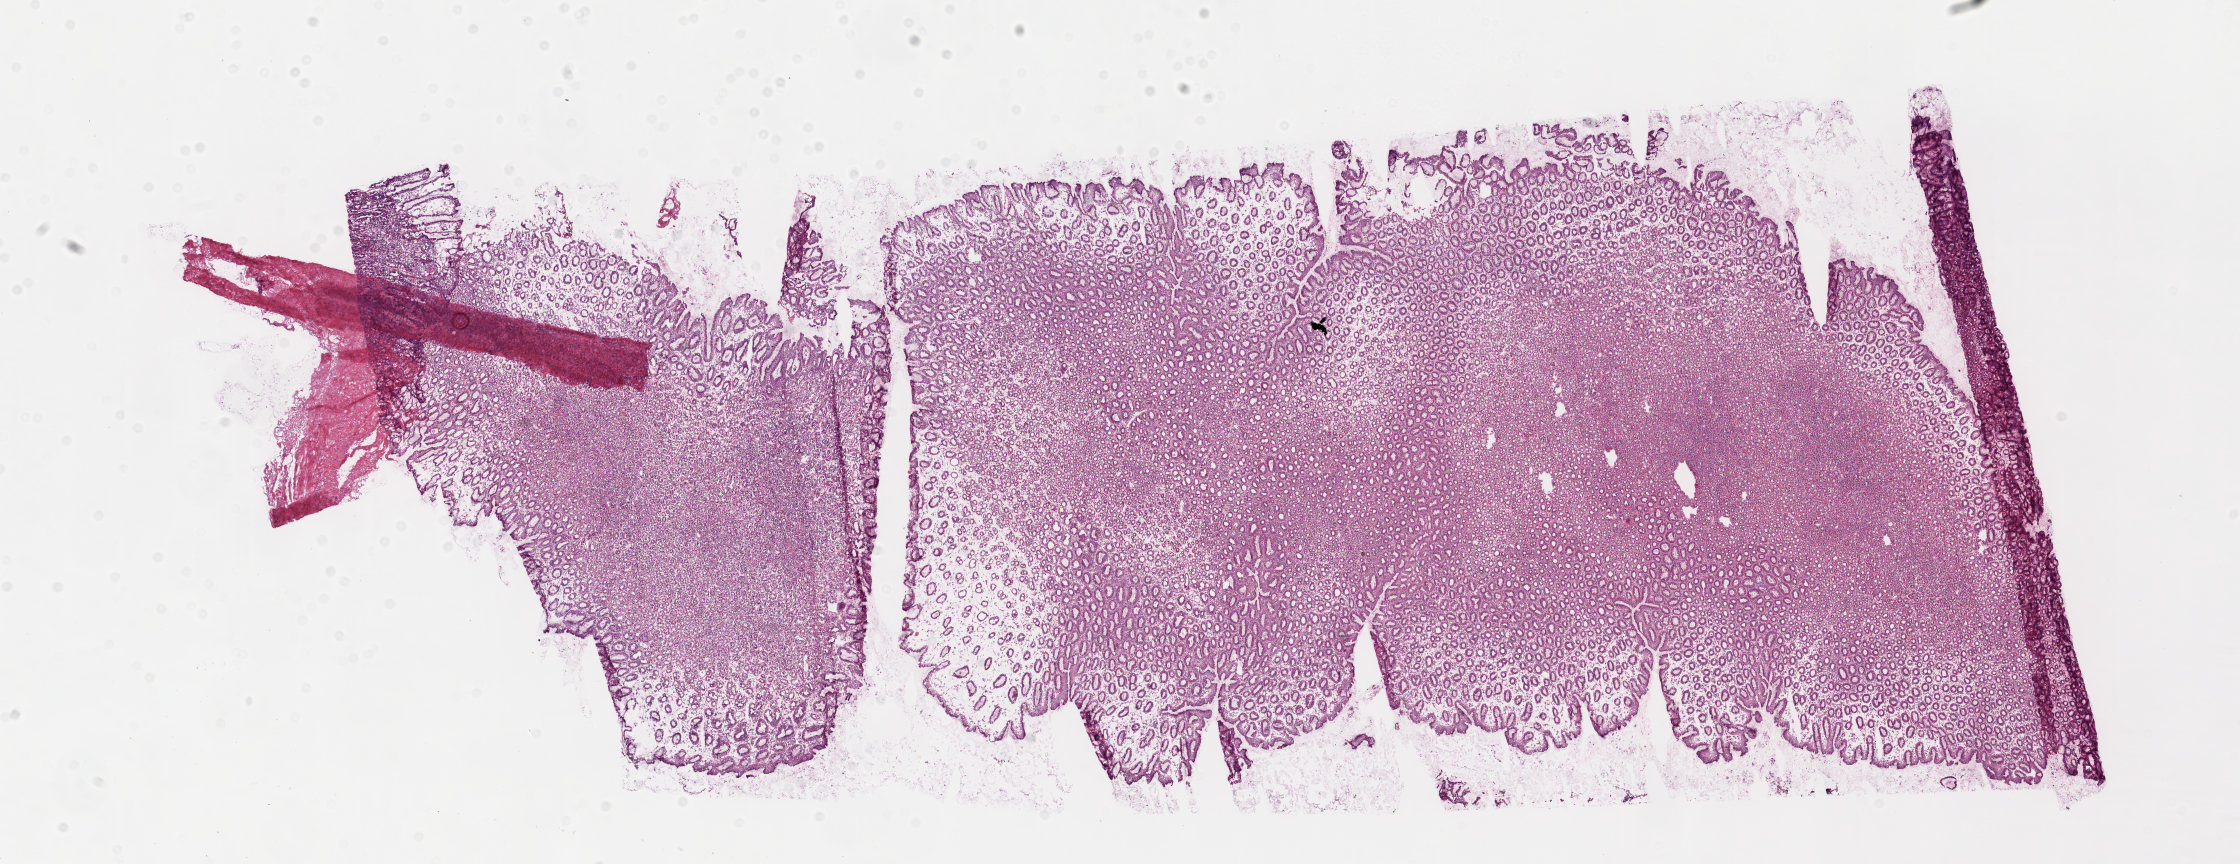
H&E whole-slide image, low-resolution overview of the scanned area, about 18.1 x 7.0 mm (acquisition: 20x scan); frozen section from the top of the tissue portion; solid tissue normal (non-tumour tissue) sample from the stomach. Female, age 86 years at initial diagnosis.
• this section: solid tissue normal sample (biorepository sample class)
• patient diagnosis: Adenocarcinoma, NOS